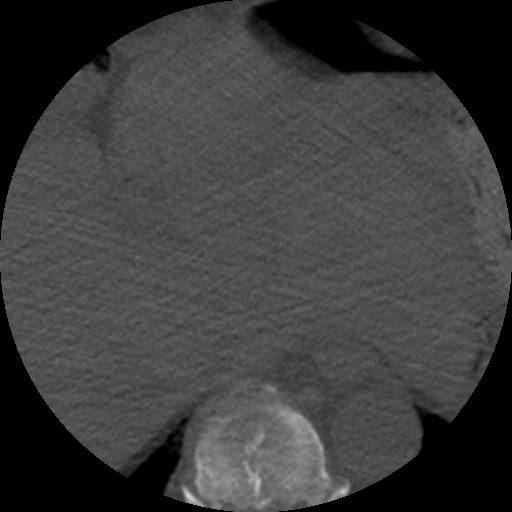
CT including the spine, one axial slice; slice 280 of 508 in the series (ordered by position); 120 kVp; bone window (W 1800 / L 400 HU); 1.25 mm slice thickness; 512 × 512 image matrix, field of view 160 × 160 mm. Patient age 57 years. Case-level facts recorded for this patient, not image findings: primary cancer: prostate.
Structures marked on this image (semi-automatically segmented with operator editing):
- T9 vertebra: box from (x=194, y=385) to (x=331, y=512) px